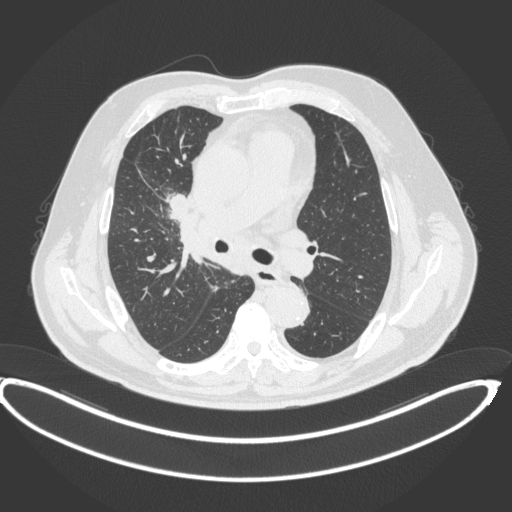
Chest CT, one axial slice. Slice 248 of 395 in the series (ordered by position). Reconstruction kernel B31f. Lung window (W 1500 / L -600 HU). 1 mm slice thickness. 512 × 512 image matrix, field of view 448 × 448 mm. Male patient, age 62 years. From the clinical record (not read from this slice): clinical TNM (as recorded): T1c N3 M1c.
Annotated regions visible in this slice (rectangle marked by the reading radiologist):
- lung tumour (recorded histology: adenocarcinoma): box from (x=164, y=191) to (x=199, y=225) px